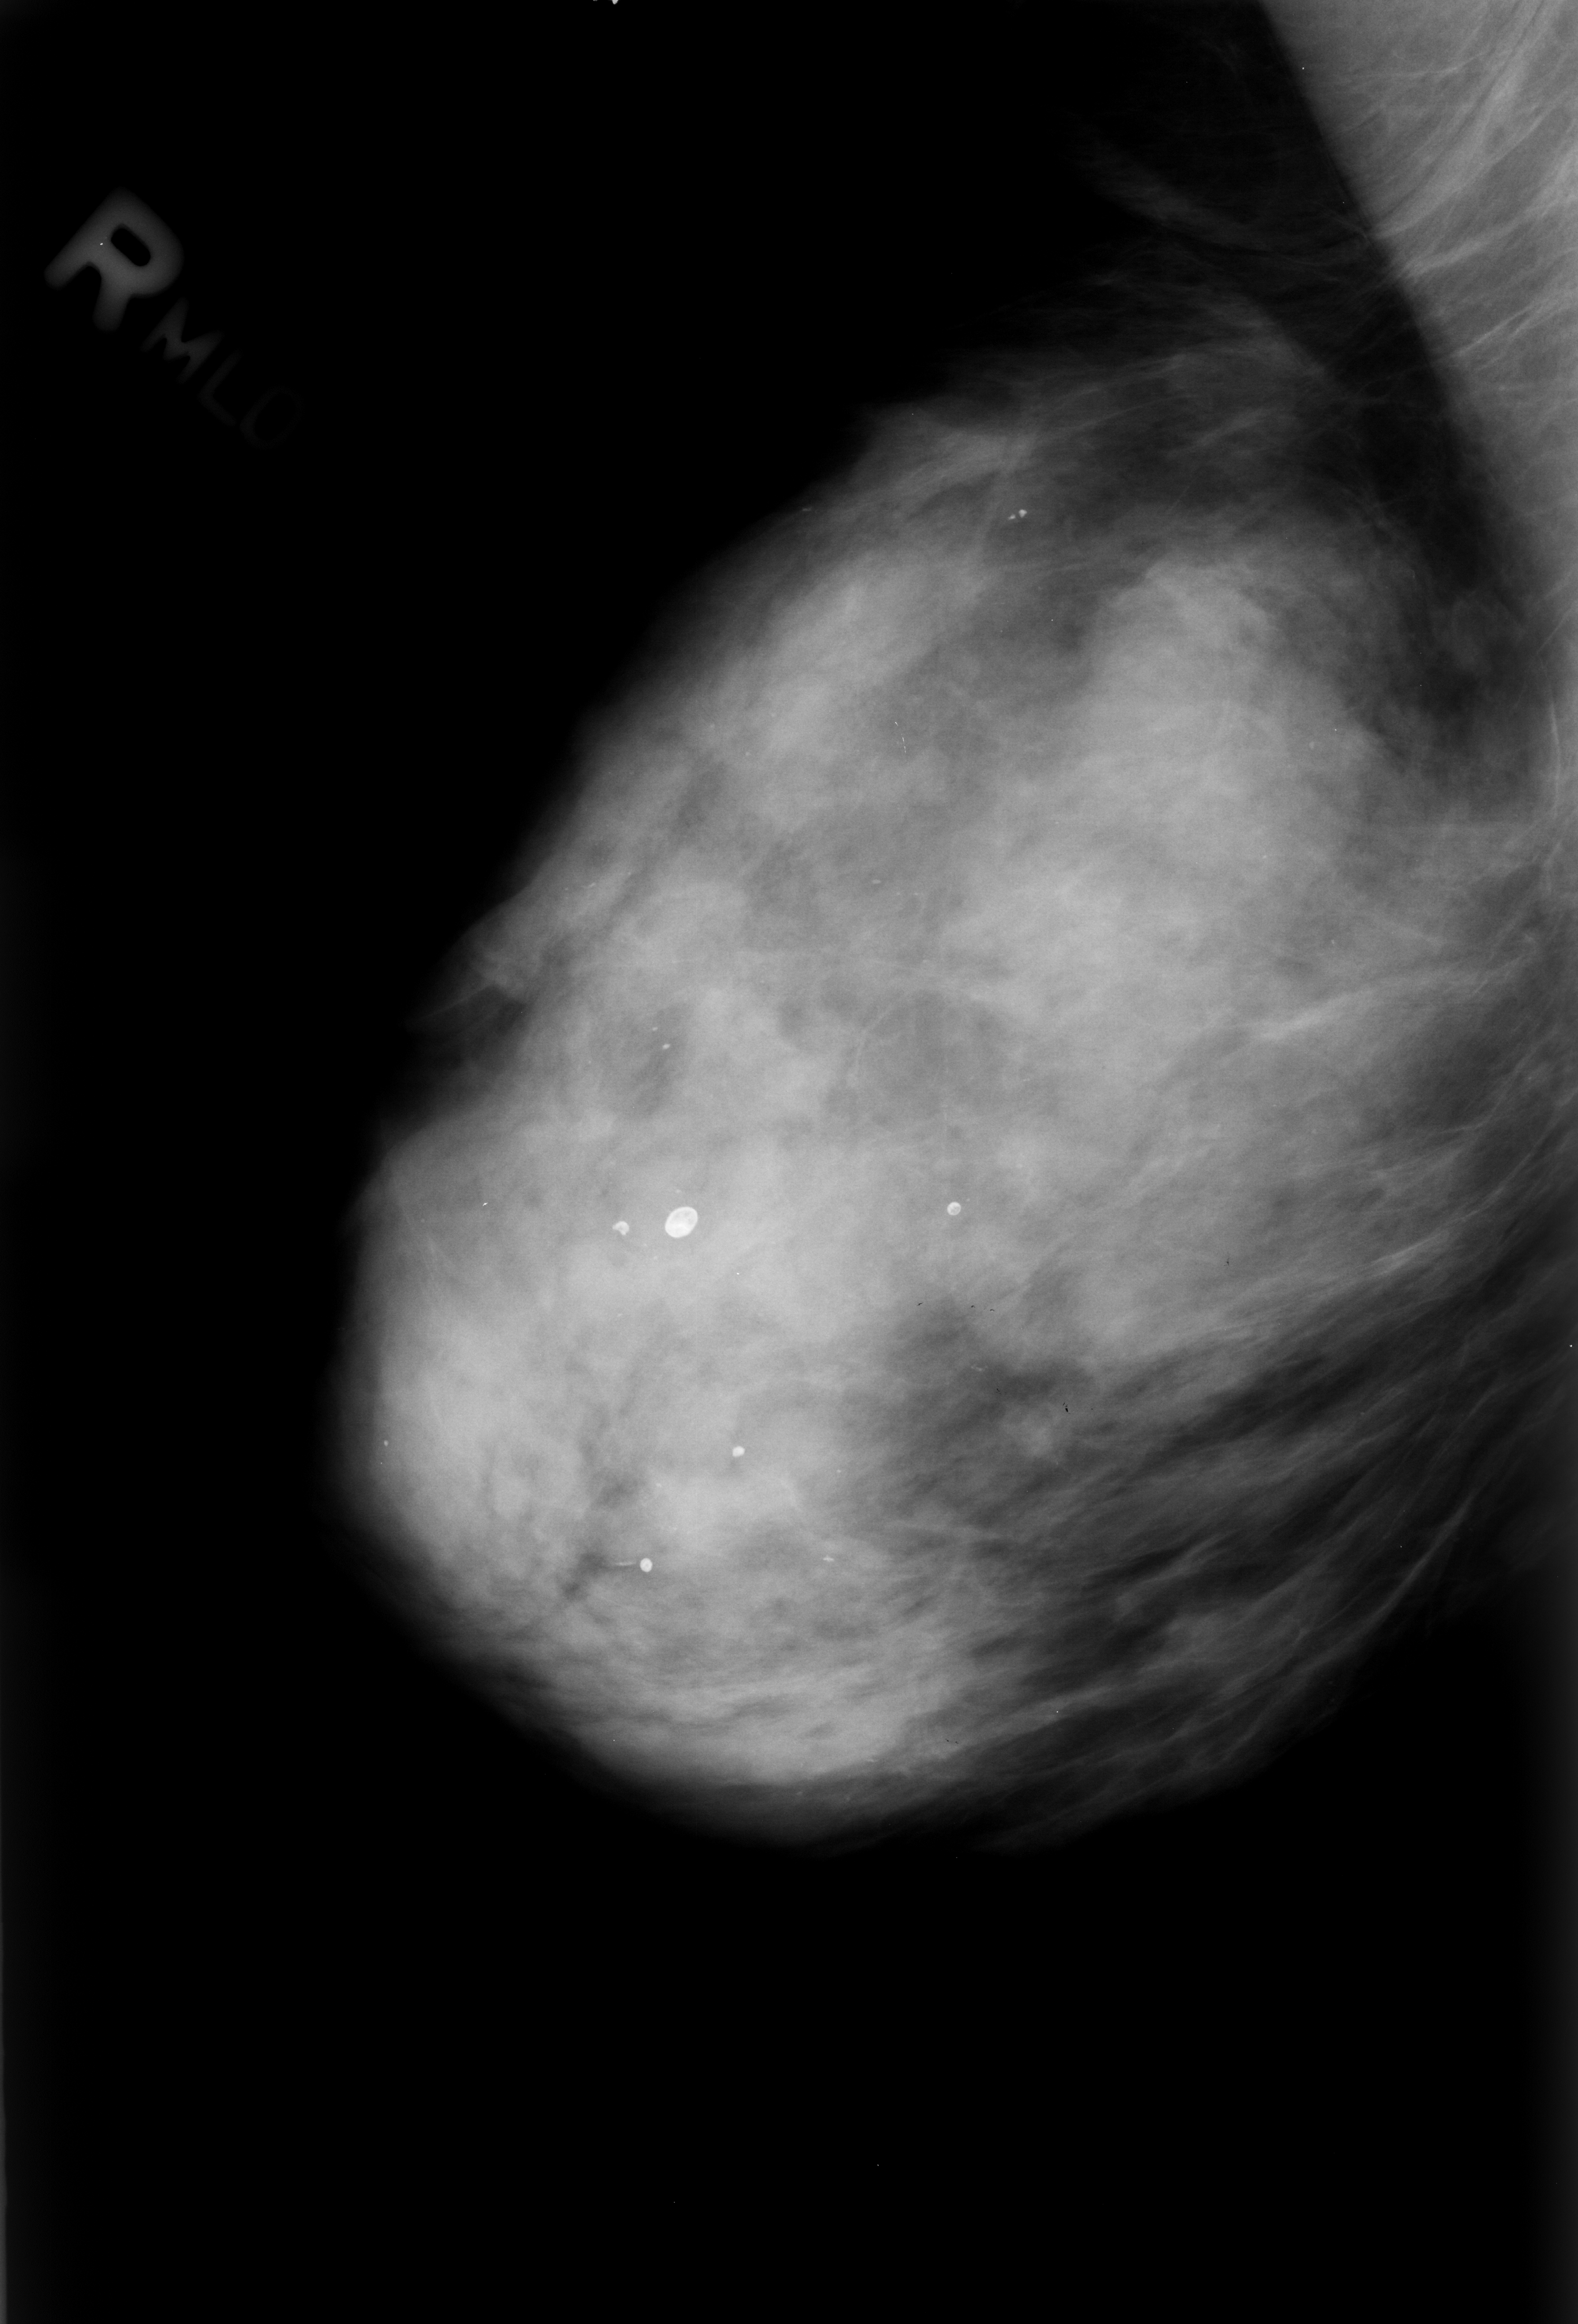
Scanned film-screen mammogram; right breast; MLO view; BI-RADS breast density category 4 (scale 1–4); 1578 × 2324 image matrix.
Expert-marked regions of interest on this film, with their recorded descriptors:
- Finding 1 of 6: calcifications, morphology round and regular / lucent center / punctate, distribution diffusely scattered; BI-RADS assessment category 2; subtlety rating 5 on a 1 (subtle) to 5 (obvious) scale; benign; no additional work-up was recommended (outcome (as recorded, no biopsy): benign without callback): bounding box [x1, y1, x2, y2] px = [598, 1212, 637, 1261]
- Finding 2 of 6: calcifications, morphology round and regular / lucent center / punctate, distribution diffusely scattered; BI-RADS assessment category 2; subtlety rating 5 on a 1 (subtle) to 5 (obvious) scale; outcome (as recorded, no biopsy): benign without callback (not worked up further): [619, 1539, 697, 1604]
- Finding 3 of 6: calcifications, morphology round and regular / lucent center / punctate, distribution diffusely scattered; BI-RADS assessment category 2; outcome (as recorded, no biopsy): benign without callback (not worked up further): [653, 1204, 722, 1261]
- Finding 4 of 6: calcifications, morphology round and regular / lucent center / punctate, distribution diffusely scattered; BI-RADS assessment category 2; outcome (as recorded, no biopsy): benign without callback (not worked up further): [716, 1429, 777, 1477]
- Finding 5 of 6: calcifications, morphology round and regular / lucent center / punctate, distribution diffusely scattered; BI-RADS assessment category 2; benign; no additional work-up was recommended (outcome (as recorded, no biopsy): benign without callback): [899, 1183, 977, 1244]
- Finding 6 of 6: calcifications, morphology round and regular / lucent center / punctate, distribution diffusely scattered; BI-RADS assessment category 2; subtlety rating 5 on a 1 (subtle) to 5 (obvious) scale; benign; no additional work-up was recommended (outcome (as recorded, no biopsy): benign without callback): [988, 491, 1074, 540]